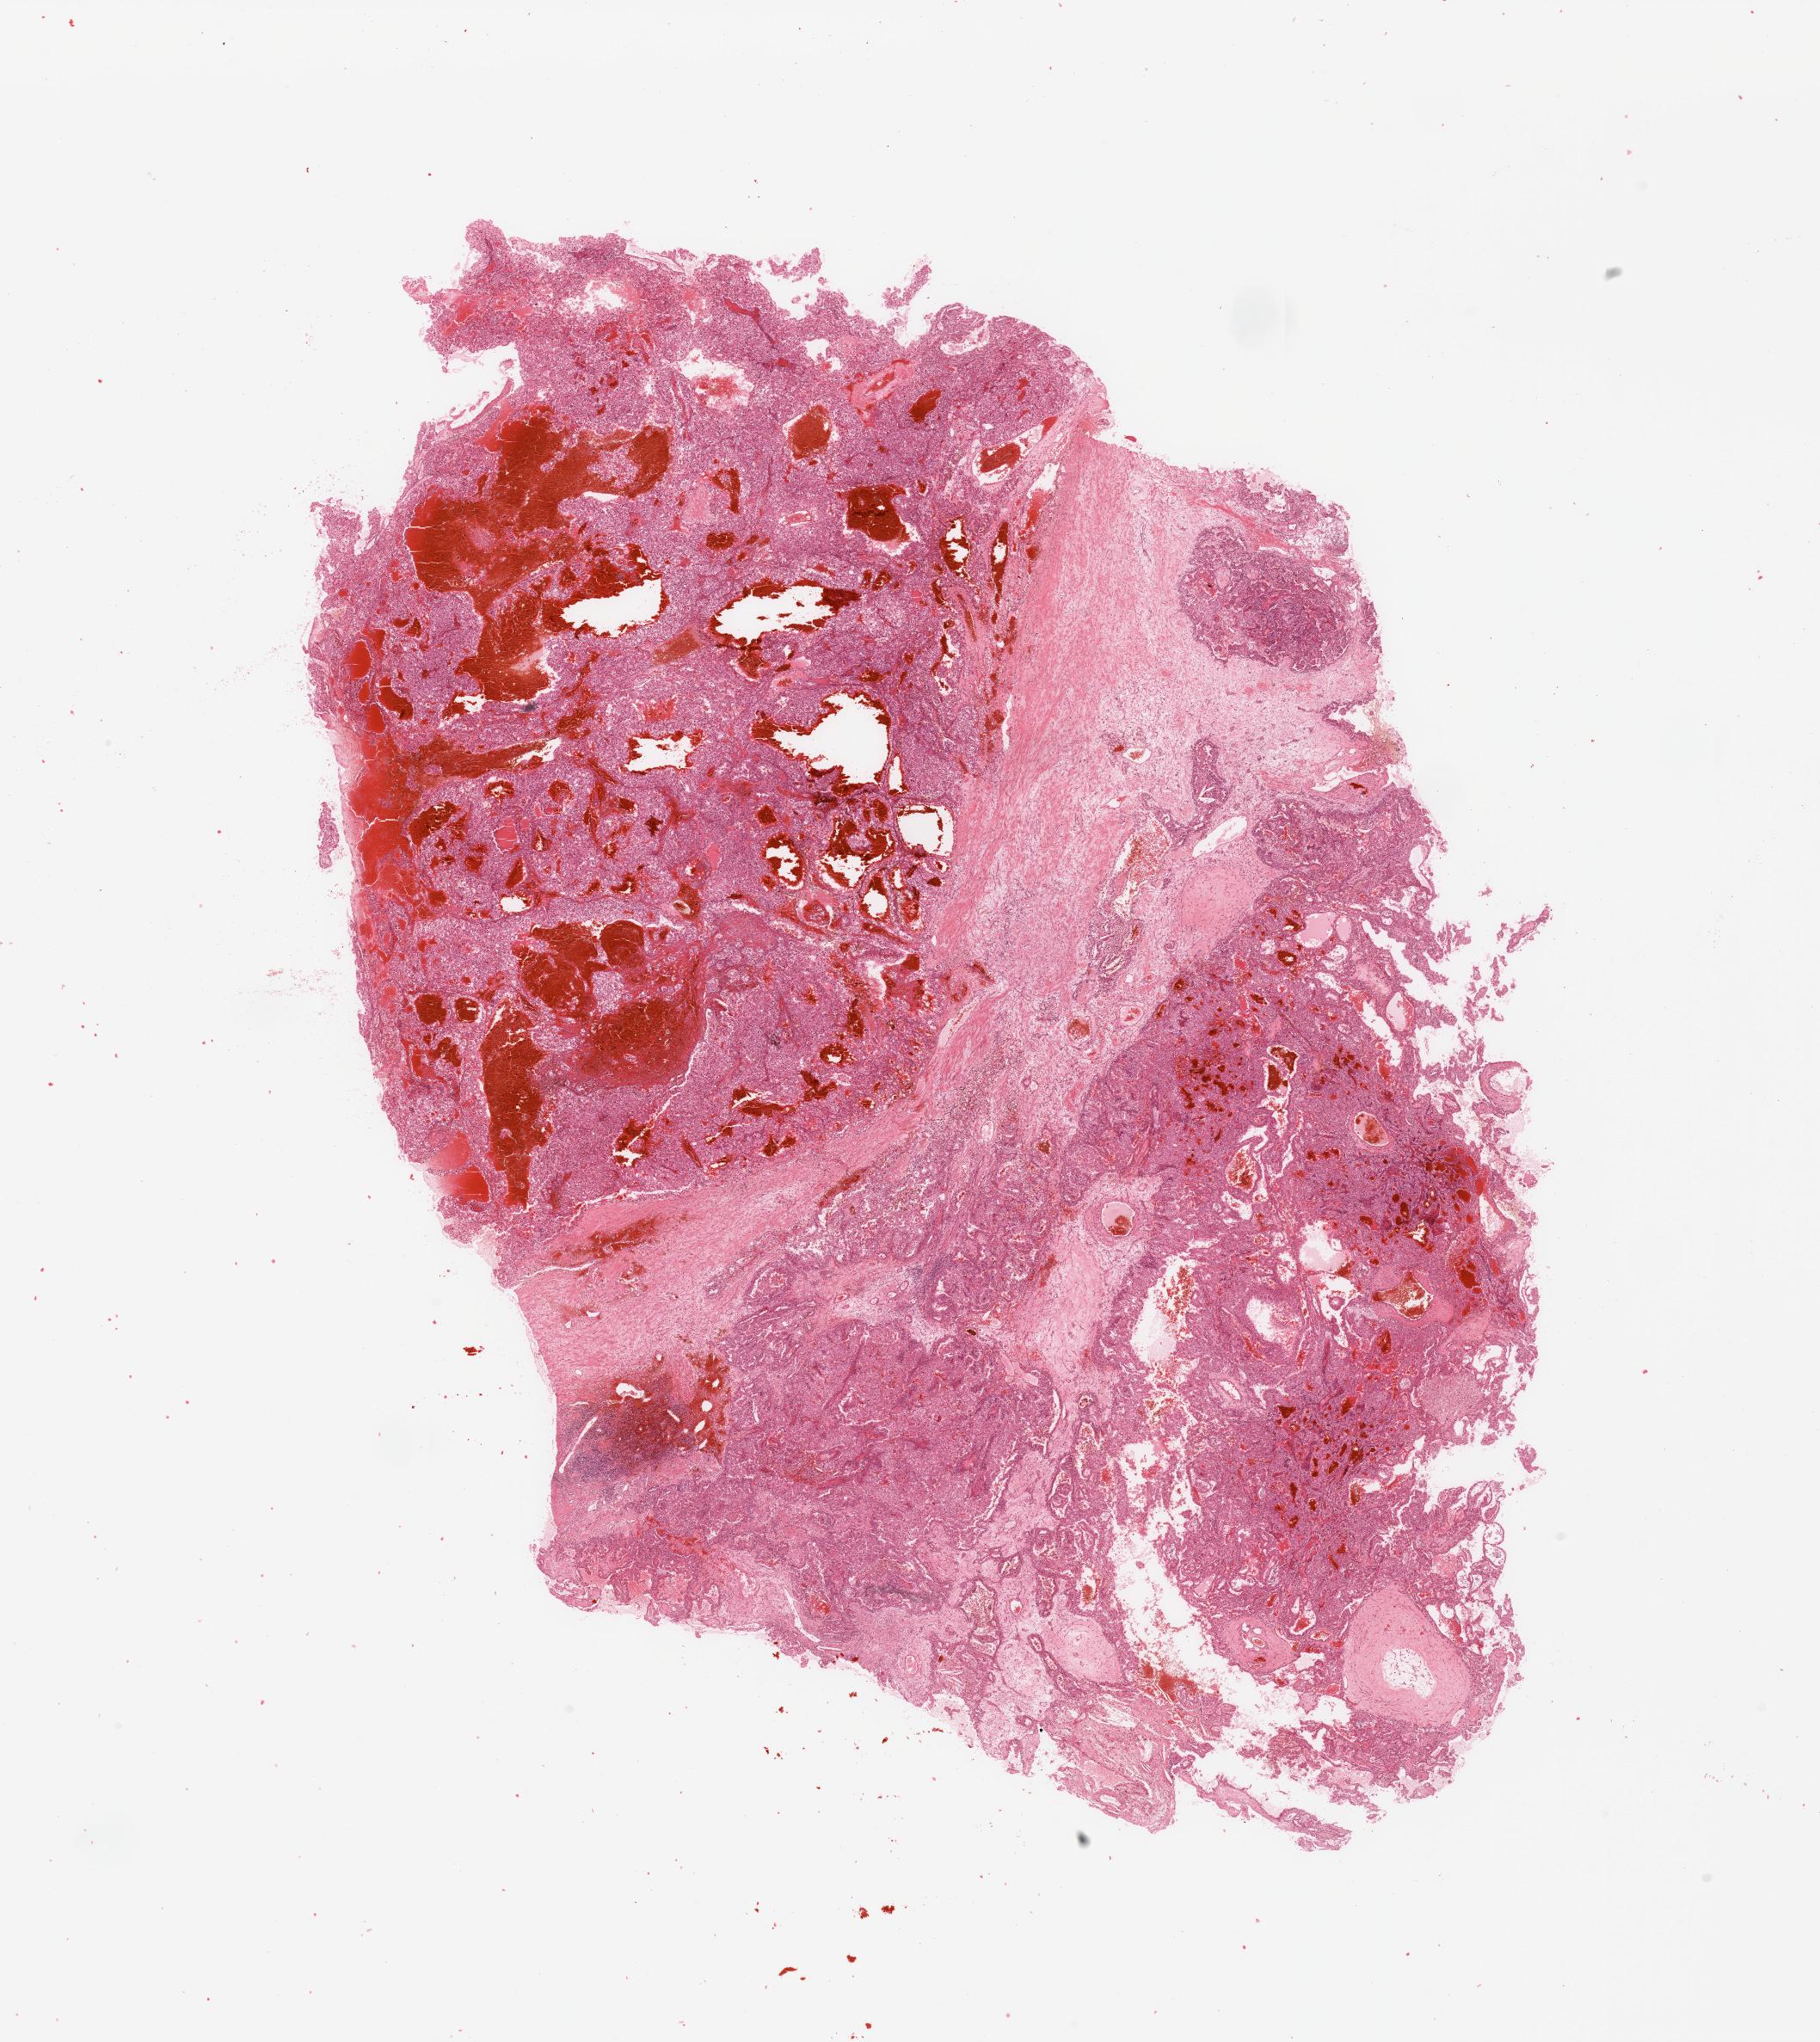
H&E whole-slide image, low-resolution overview of the scanned area, about 16.7 x 18.8 mm; tumour tissue sample, sampled site: kidney. Male, 52 y/o. Histologic grade: G2 (moderately differentiated). Pathologist review of this section (percent, as recorded): tumour nuclei 80%, necrosis 10%.
AJCC pathologic stage: III. Diagnosis: Renal cell carcinoma, NOS.